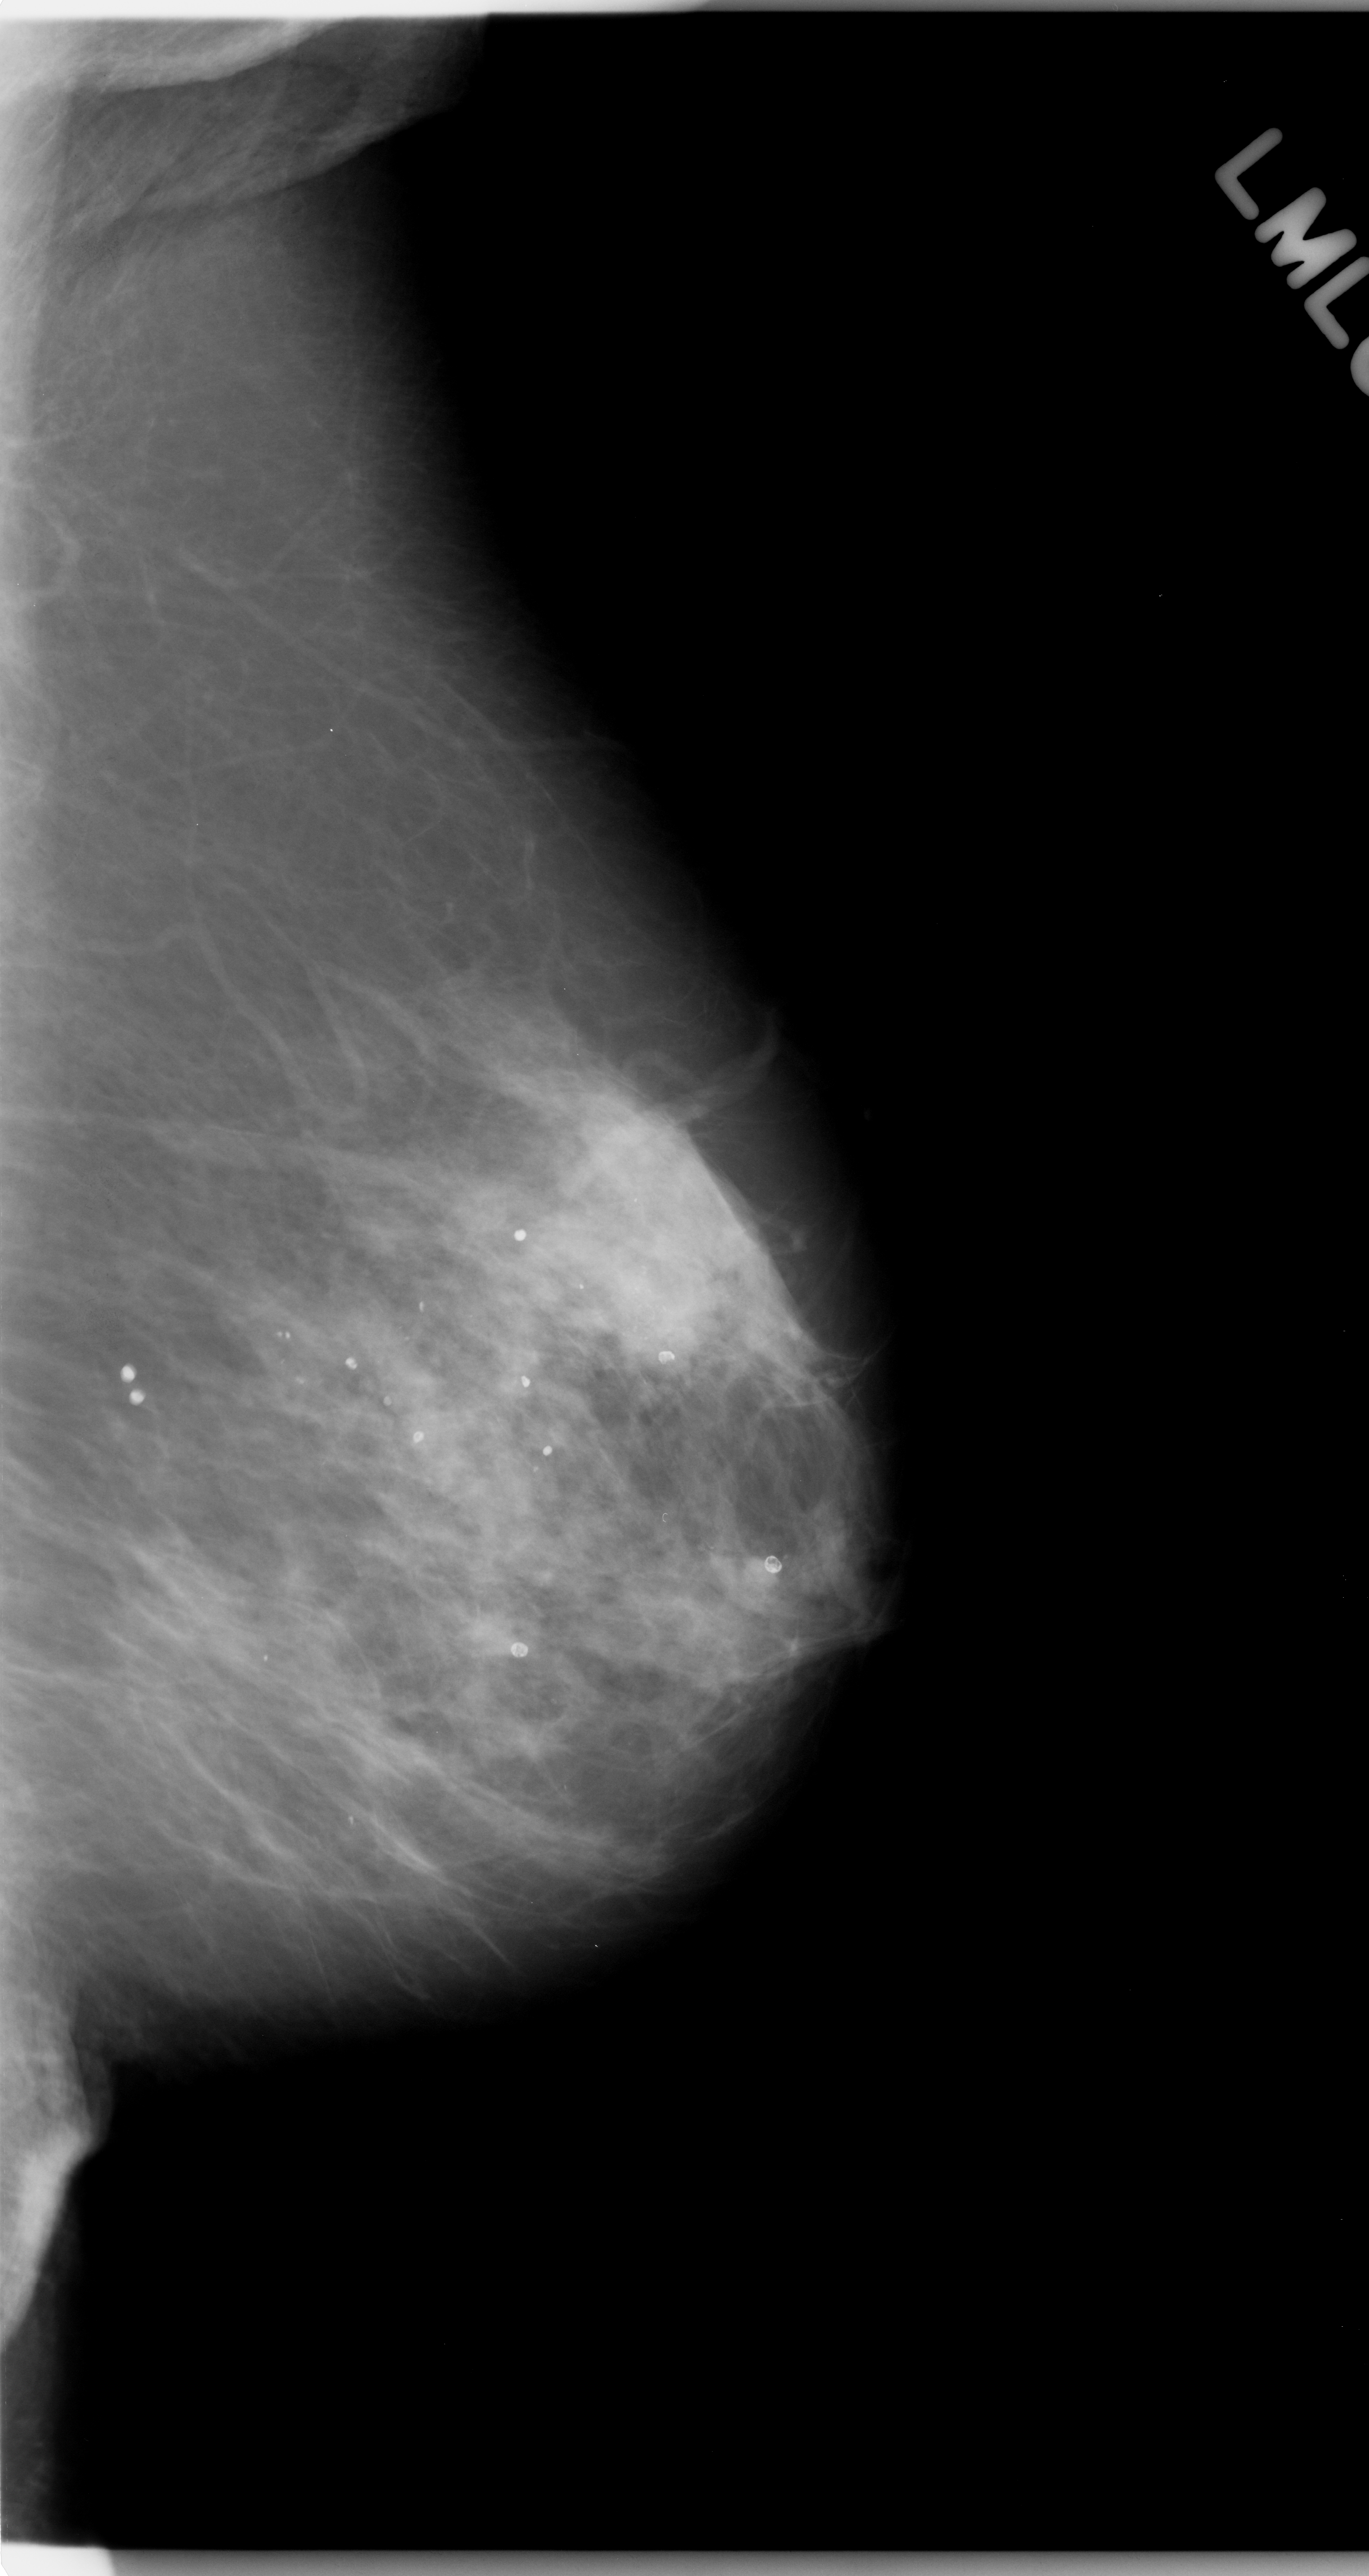
Digitized screen-film mammogram, left breast, mediolateral oblique (MLO) view, BI-RADS breast density category 2 (scale 1–4).
Abnormality record for this image: calcifications, morphology amorphous, distribution clustered; BI-RADS assessment category 5; pathology (as recorded): malignant.